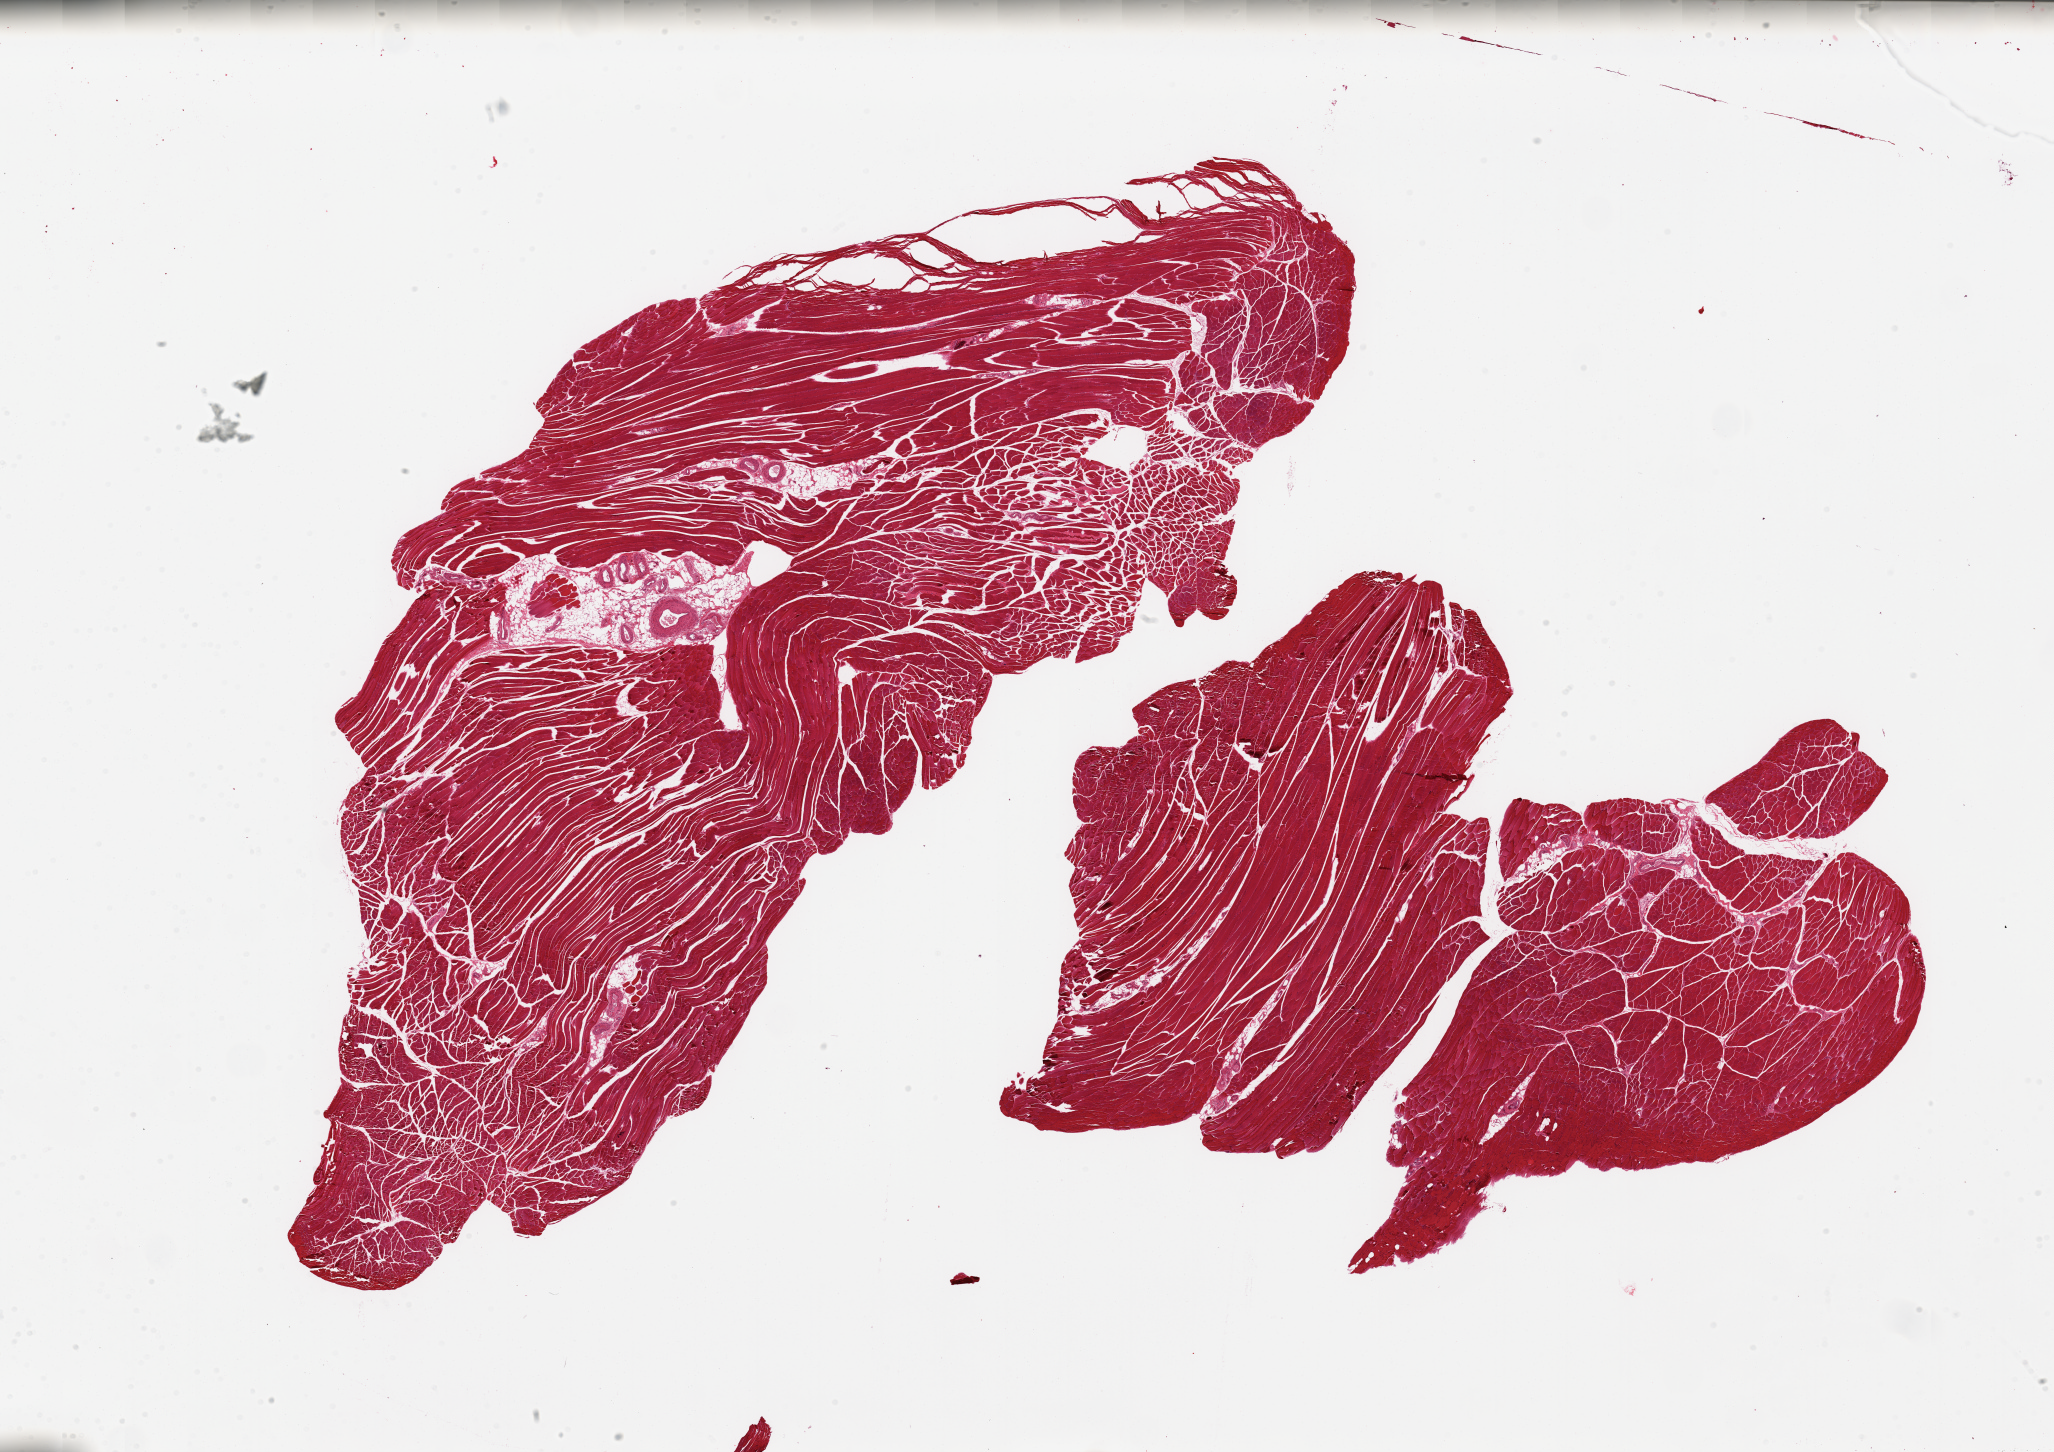
Hematoxylin and eosin (H&E) whole-slide image, brightfield — low-resolution overview of the scanned area, about 32.5 x 23.0 mm. PAXgene-fixed paraffin-embedded (PFPE) section. Section of skeletal muscle (target tissue). Tissue donor sample. Male donor.
* review note (as recorded): 2 pieces, over-sized